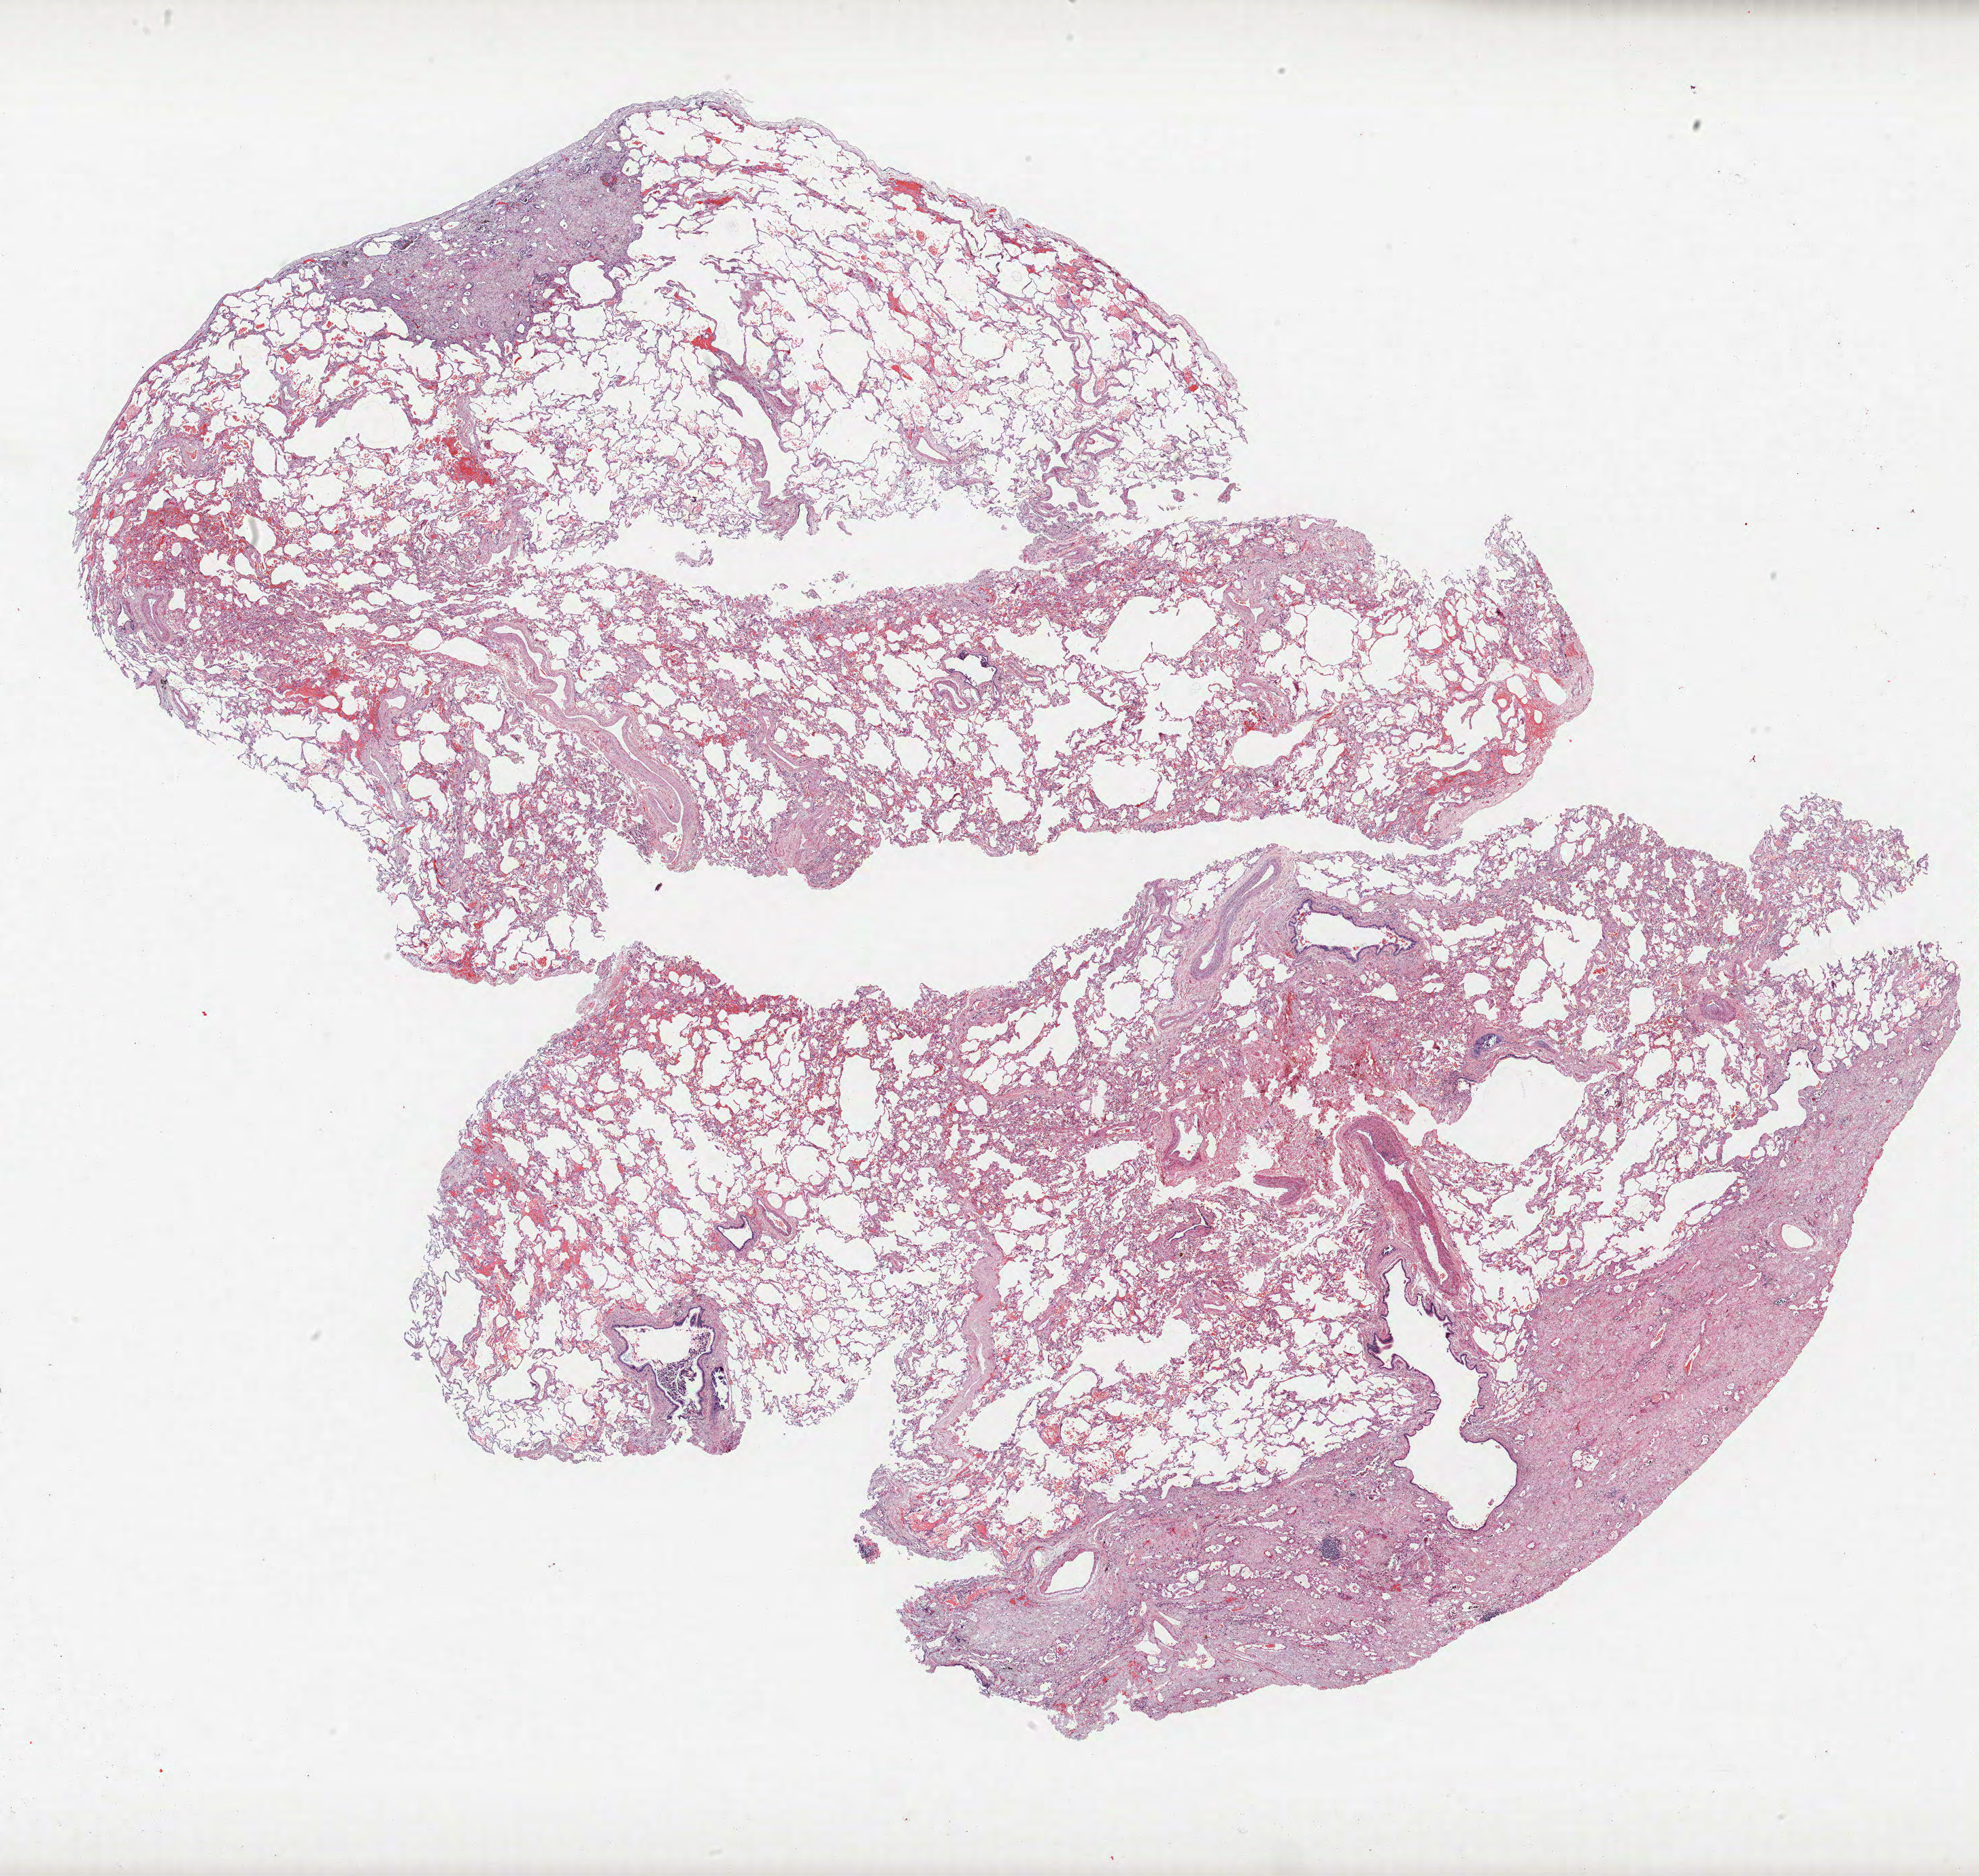
Whole-slide histology image, Hematoxylin and eosin (H&E) stained, whole scanned area (about 23.3 x 22.1 mm) shown as a low-resolution overview, formalin-fixed paraffin-embedded (FFPE) section, lung. Female patient, aged 56 at enrolment. Grade: moderately differentiated (G2).
ICD-O-3 topography: upper lobe of lung (C34.1). Tumour size (pathology): 19 mm. Stage (AJCC 6th edition): IA. Primary tumour location (clinical record): right upper lobe. Participant's lung-cancer diagnosis: Adenocarcinoma, NOS.